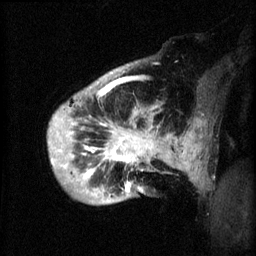
Breast MRI (dynamic contrast-enhanced), one sagittal slice; position 8 of 60 along the scan axis; 3 images stored at this slice position (order not interpretable as contrast timing); 1.5 T; TE 4.2 ms, TR 8.2 ms; 2 mm slice thickness; 256 × 256 image matrix. Female patient, age 50 years.
Outlined on this slice (semi-automatically segmented with operator editing):
- analysis volume of interest (the breast-tissue region the enhancement analysis was run in; not a lesion): bounding box (x1, y1, x2, y2) in pixels: (48, 72, 173, 205)
- tumour enhancement mask (voxels above the 70 % enhancement threshold inside the analysis volume of interest): (49, 82, 173, 193)